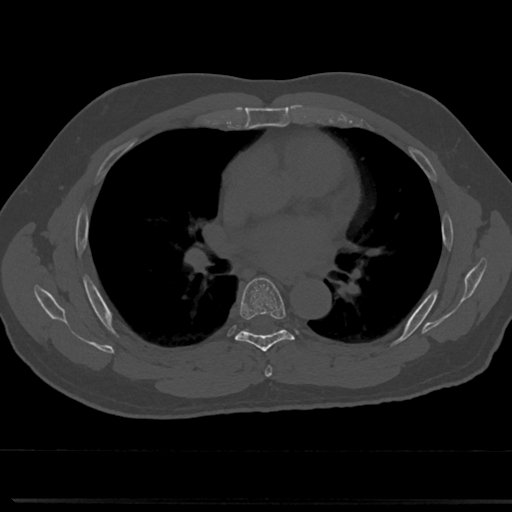
CT including the spine, one axial slice; position 451 of 817 along the scan axis; 120 kVp; bone window (W 1800 / L 400 HU); 0.5 mm slice thickness; 512 × 512 image matrix, field of view 355 × 355 mm. Patient: male, 61 years. From the clinical record (not read from this slice): primary cancer: prostate.
Annotated regions visible in this slice (semi-automatic segmentation, software-assisted and operator-edited):
- T5 vertebra: box from (x=263, y=347) to (x=273, y=374) px
- T6 vertebra: (x=218, y=277)–(x=311, y=355)